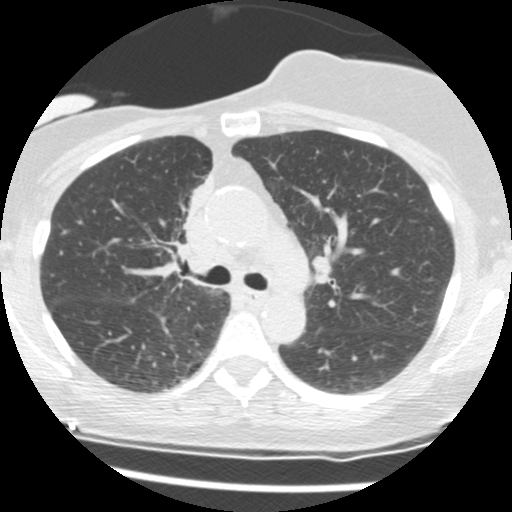
Axial slice from a low-dose chest CT screening exam. Second annual screen. Lung window (W 1500 / L -600 HU). 2.5 mm slice thickness. Standard (soft-tissue) reconstruction kernel (STANDARD). Slice 48 of 165 in the series. 512 × 512 image matrix, field of view 296 × 296 mm. Female participant, aged 56 years at enrolment. Current smoker at enrolment.
Expert reader's lesion annotation, bounding box (x1, y1, x2, y2) in pixels: (153, 176, 210, 264). The screening reader recorded 2 non-calcified nodules or masses ≥4 mm on this exam (right middle lobe, right lower lobe); which of them this box marks is not recorded. Official screen result: positive, change unspecified: nodule(s) >= 4 mm or enlarging nodule(s), mass(es), or other non-specific abnormalities suspicious for lung cancer. Participant outcome: lung cancer diagnosed 675 days after this screen — adenocarcinoma, NOS, right upper lobe, stage IIIB (AJCC 6th edition), 8 mm at pathology.